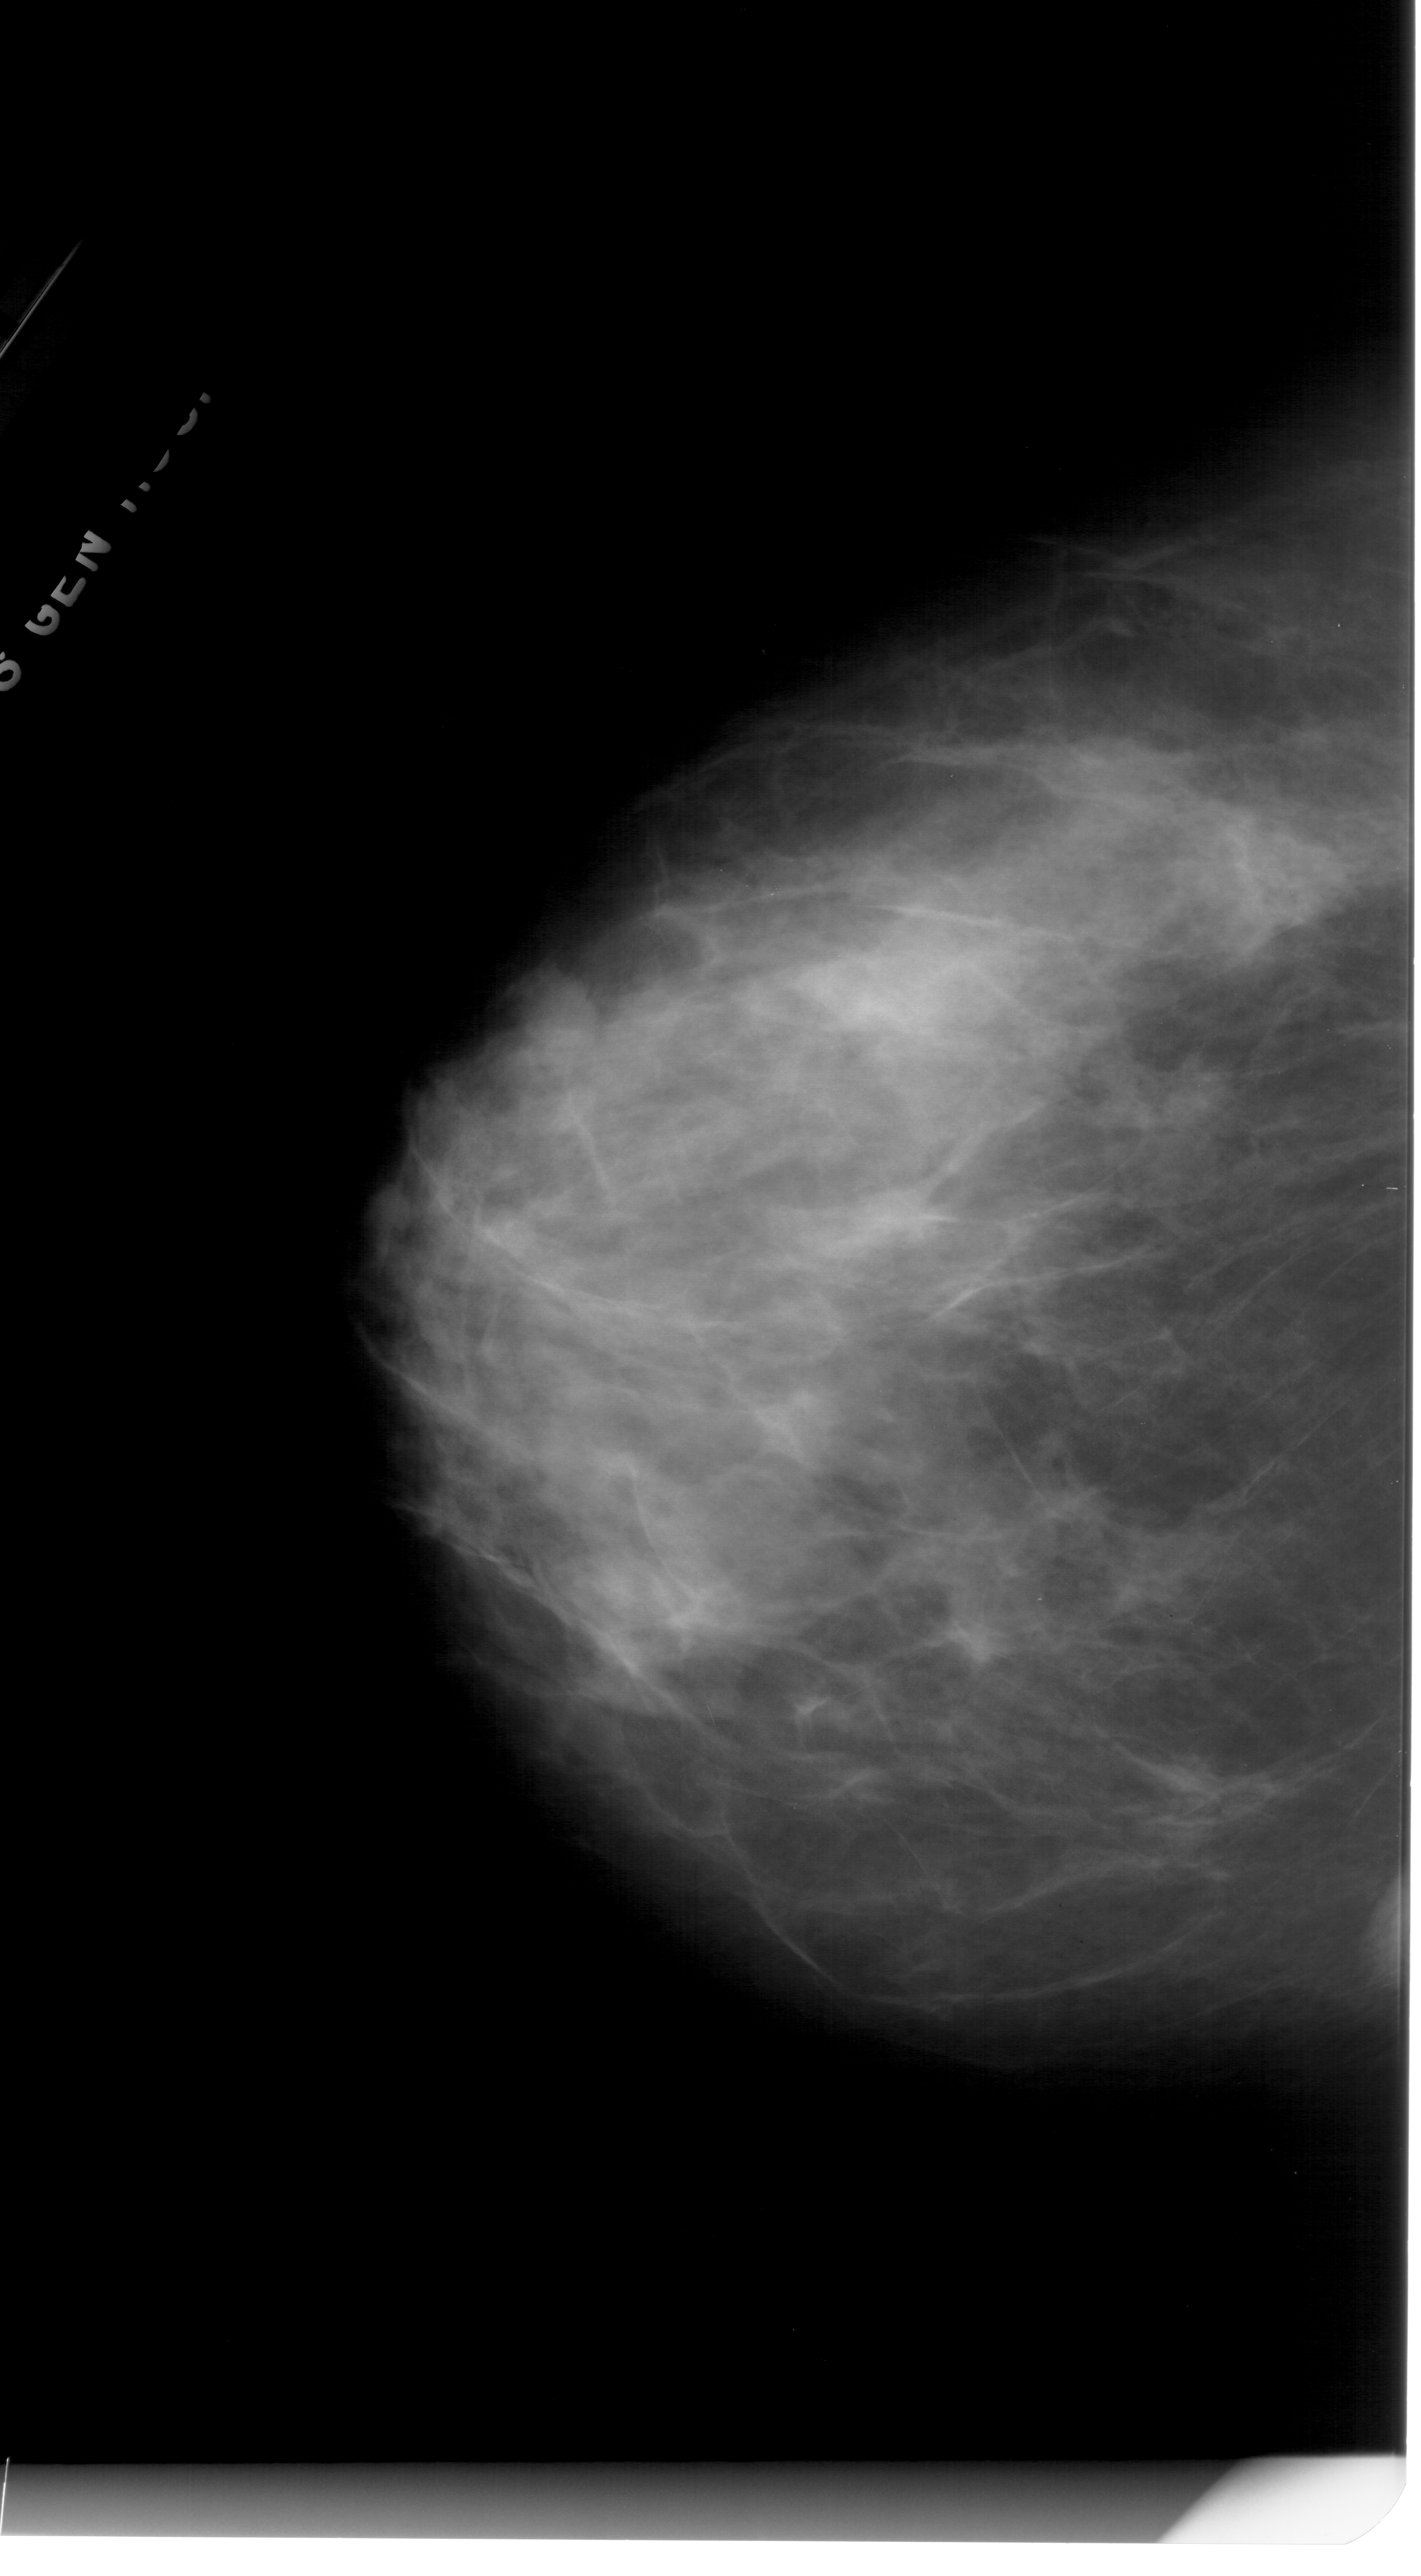
Mammogram (digitized film); left breast; craniocaudal (CC) view; breast composition: extremely dense (BI-RADS density category 4 of 4); 1421 × 2576 image matrix.
Marked abnormalities (boxes around the expert regions of interest):
- mass, shape oval, margins ill defined; BI-RADS assessment category 4; pathology result (as recorded, not read from the image): benign: box from (x=516, y=964) to (x=594, y=1043) px